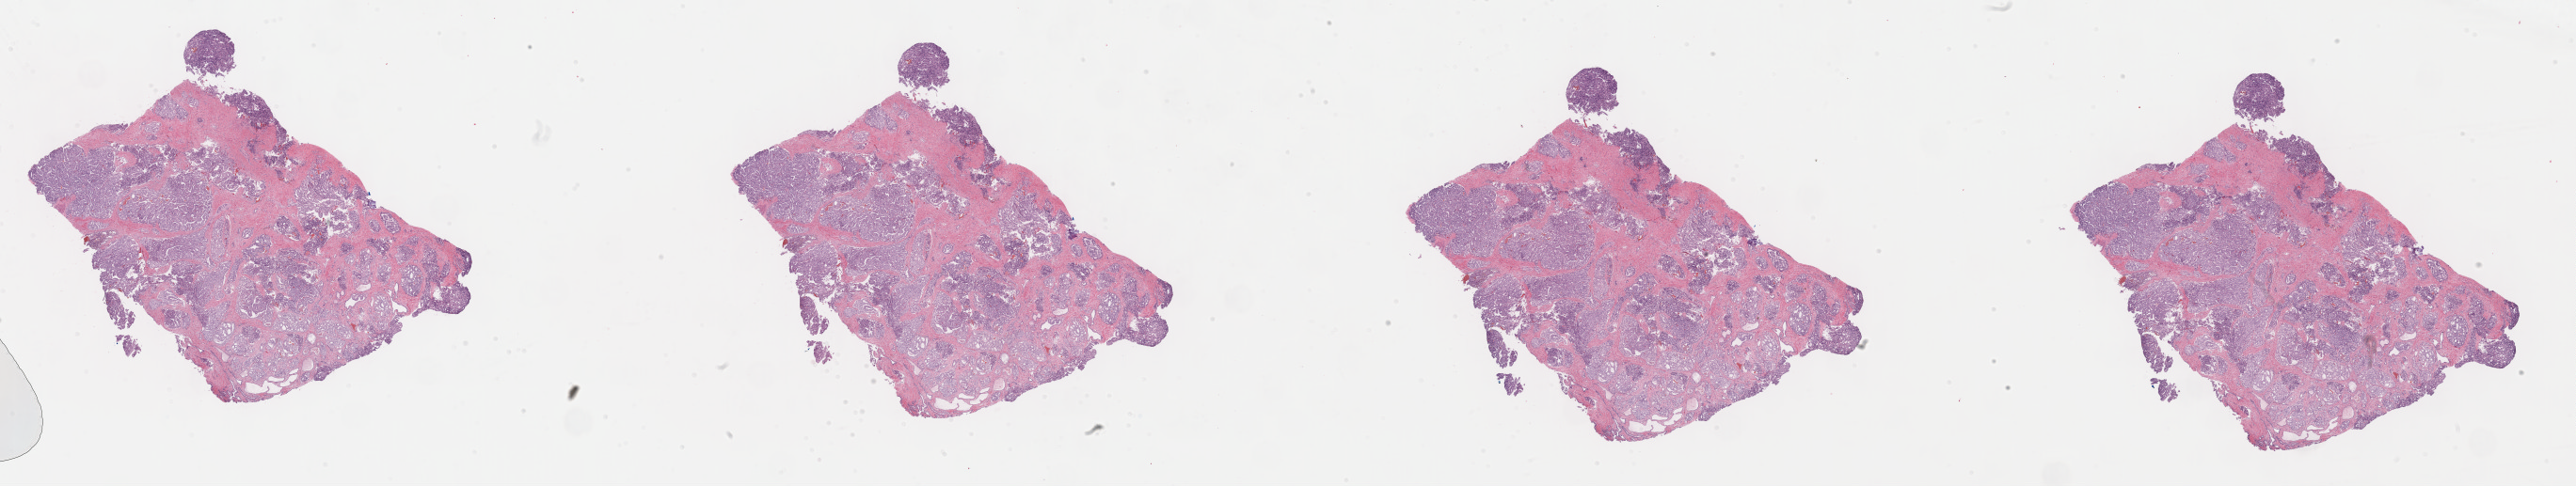
Digitized H&E tissue section (whole slide) — low-resolution overview of the scanned area, about 44.3 x 8.4 mm; formalin-fixed paraffin-embedded (FFPE) diagnostic section; prostate, primary tumour sample. Male, age 62 years at initial diagnosis. Gleason score: 7 (4+3).
Diagnosis: Adenocarcinoma, NOS (prostate gland). Lymph nodes positive (case pathology): 0 of 7 examined.